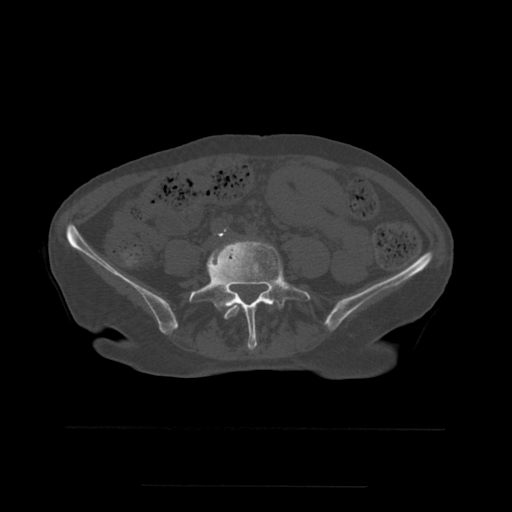
CT including the spine, one axial slice. Position 151 of 544 along the scan axis. Bone window (W 1800 / L 400 HU). 1.25 mm slice thickness. 512 × 512 image matrix. Patient age 58 years. From the clinical record (not read from this slice): primary cancer: lung.
Structures marked on this image (semi-automatic segmentation, software-assisted and operator-edited):
- L4 vertebra: box from (x=213, y=249) to (x=240, y=320) px
- L5 vertebra: (x=189, y=242)–(x=302, y=350)